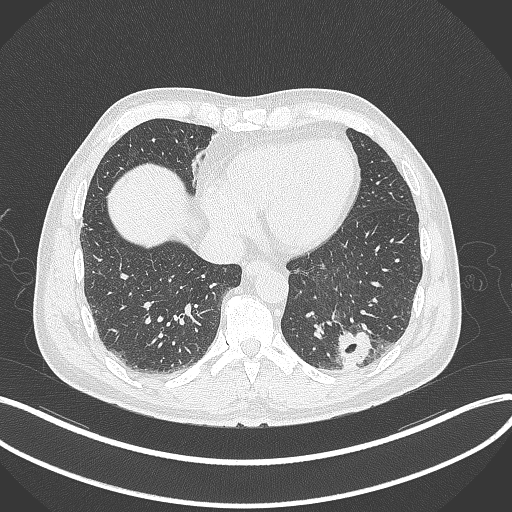
Chest CT, one axial slice. Slice 81 of 300 in the series (ordered by position). 120 kVp. Lung window (W 1500 / L -600 HU). 1 mm slice thickness. 512 × 512 image matrix. Male patient, age 54 years. From the clinical record (not read from this slice): clinical TNM (as recorded): T1c N0 M1.
Annotated regions visible in this slice (bounding box drawn by a radiologist):
- lung tumour (recorded histology: adenocarcinoma): bounding box [x1, y1, x2, y2] px = [335, 325, 373, 368]